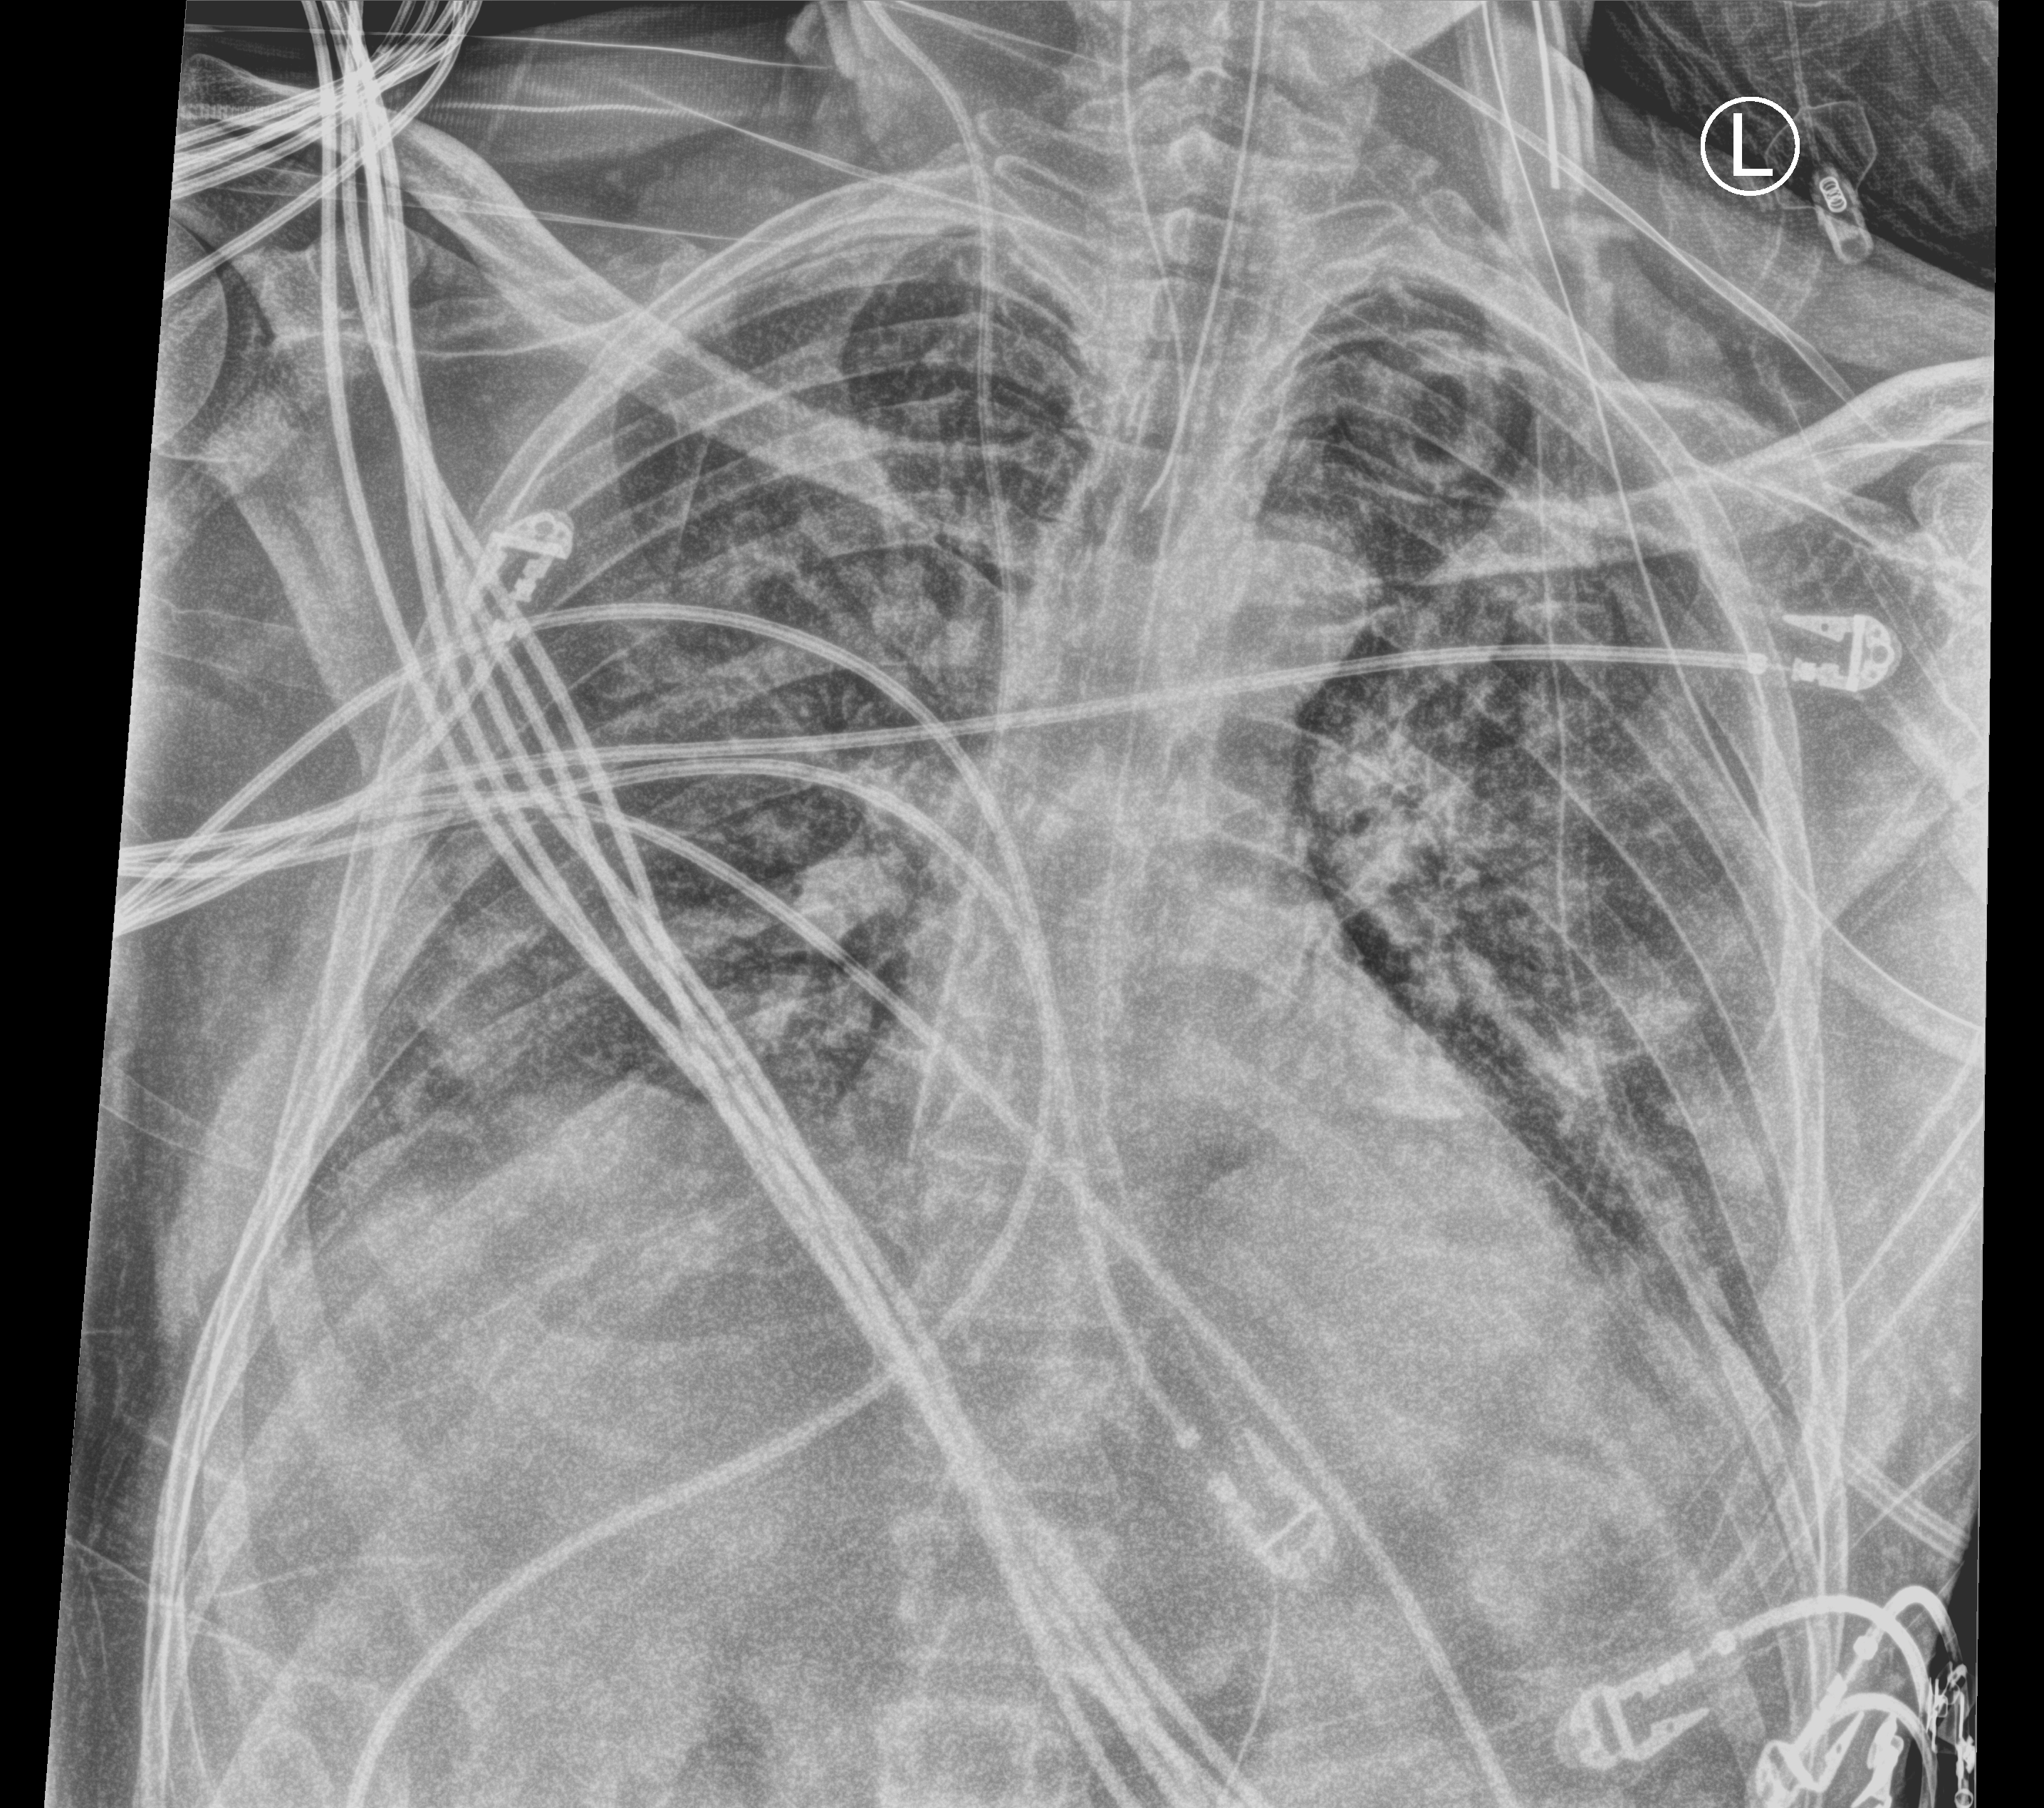
Portable chest radiograph; anteroposterior (AP) projection. Male patient hospitalised with COVID-19, age 18–59 years.
Admission-level facts for this patient (not findings on this image; timing relative to this image not recorded):
- hypertension (admission record): no
- admitted to intensive care during this hospital stay: yes